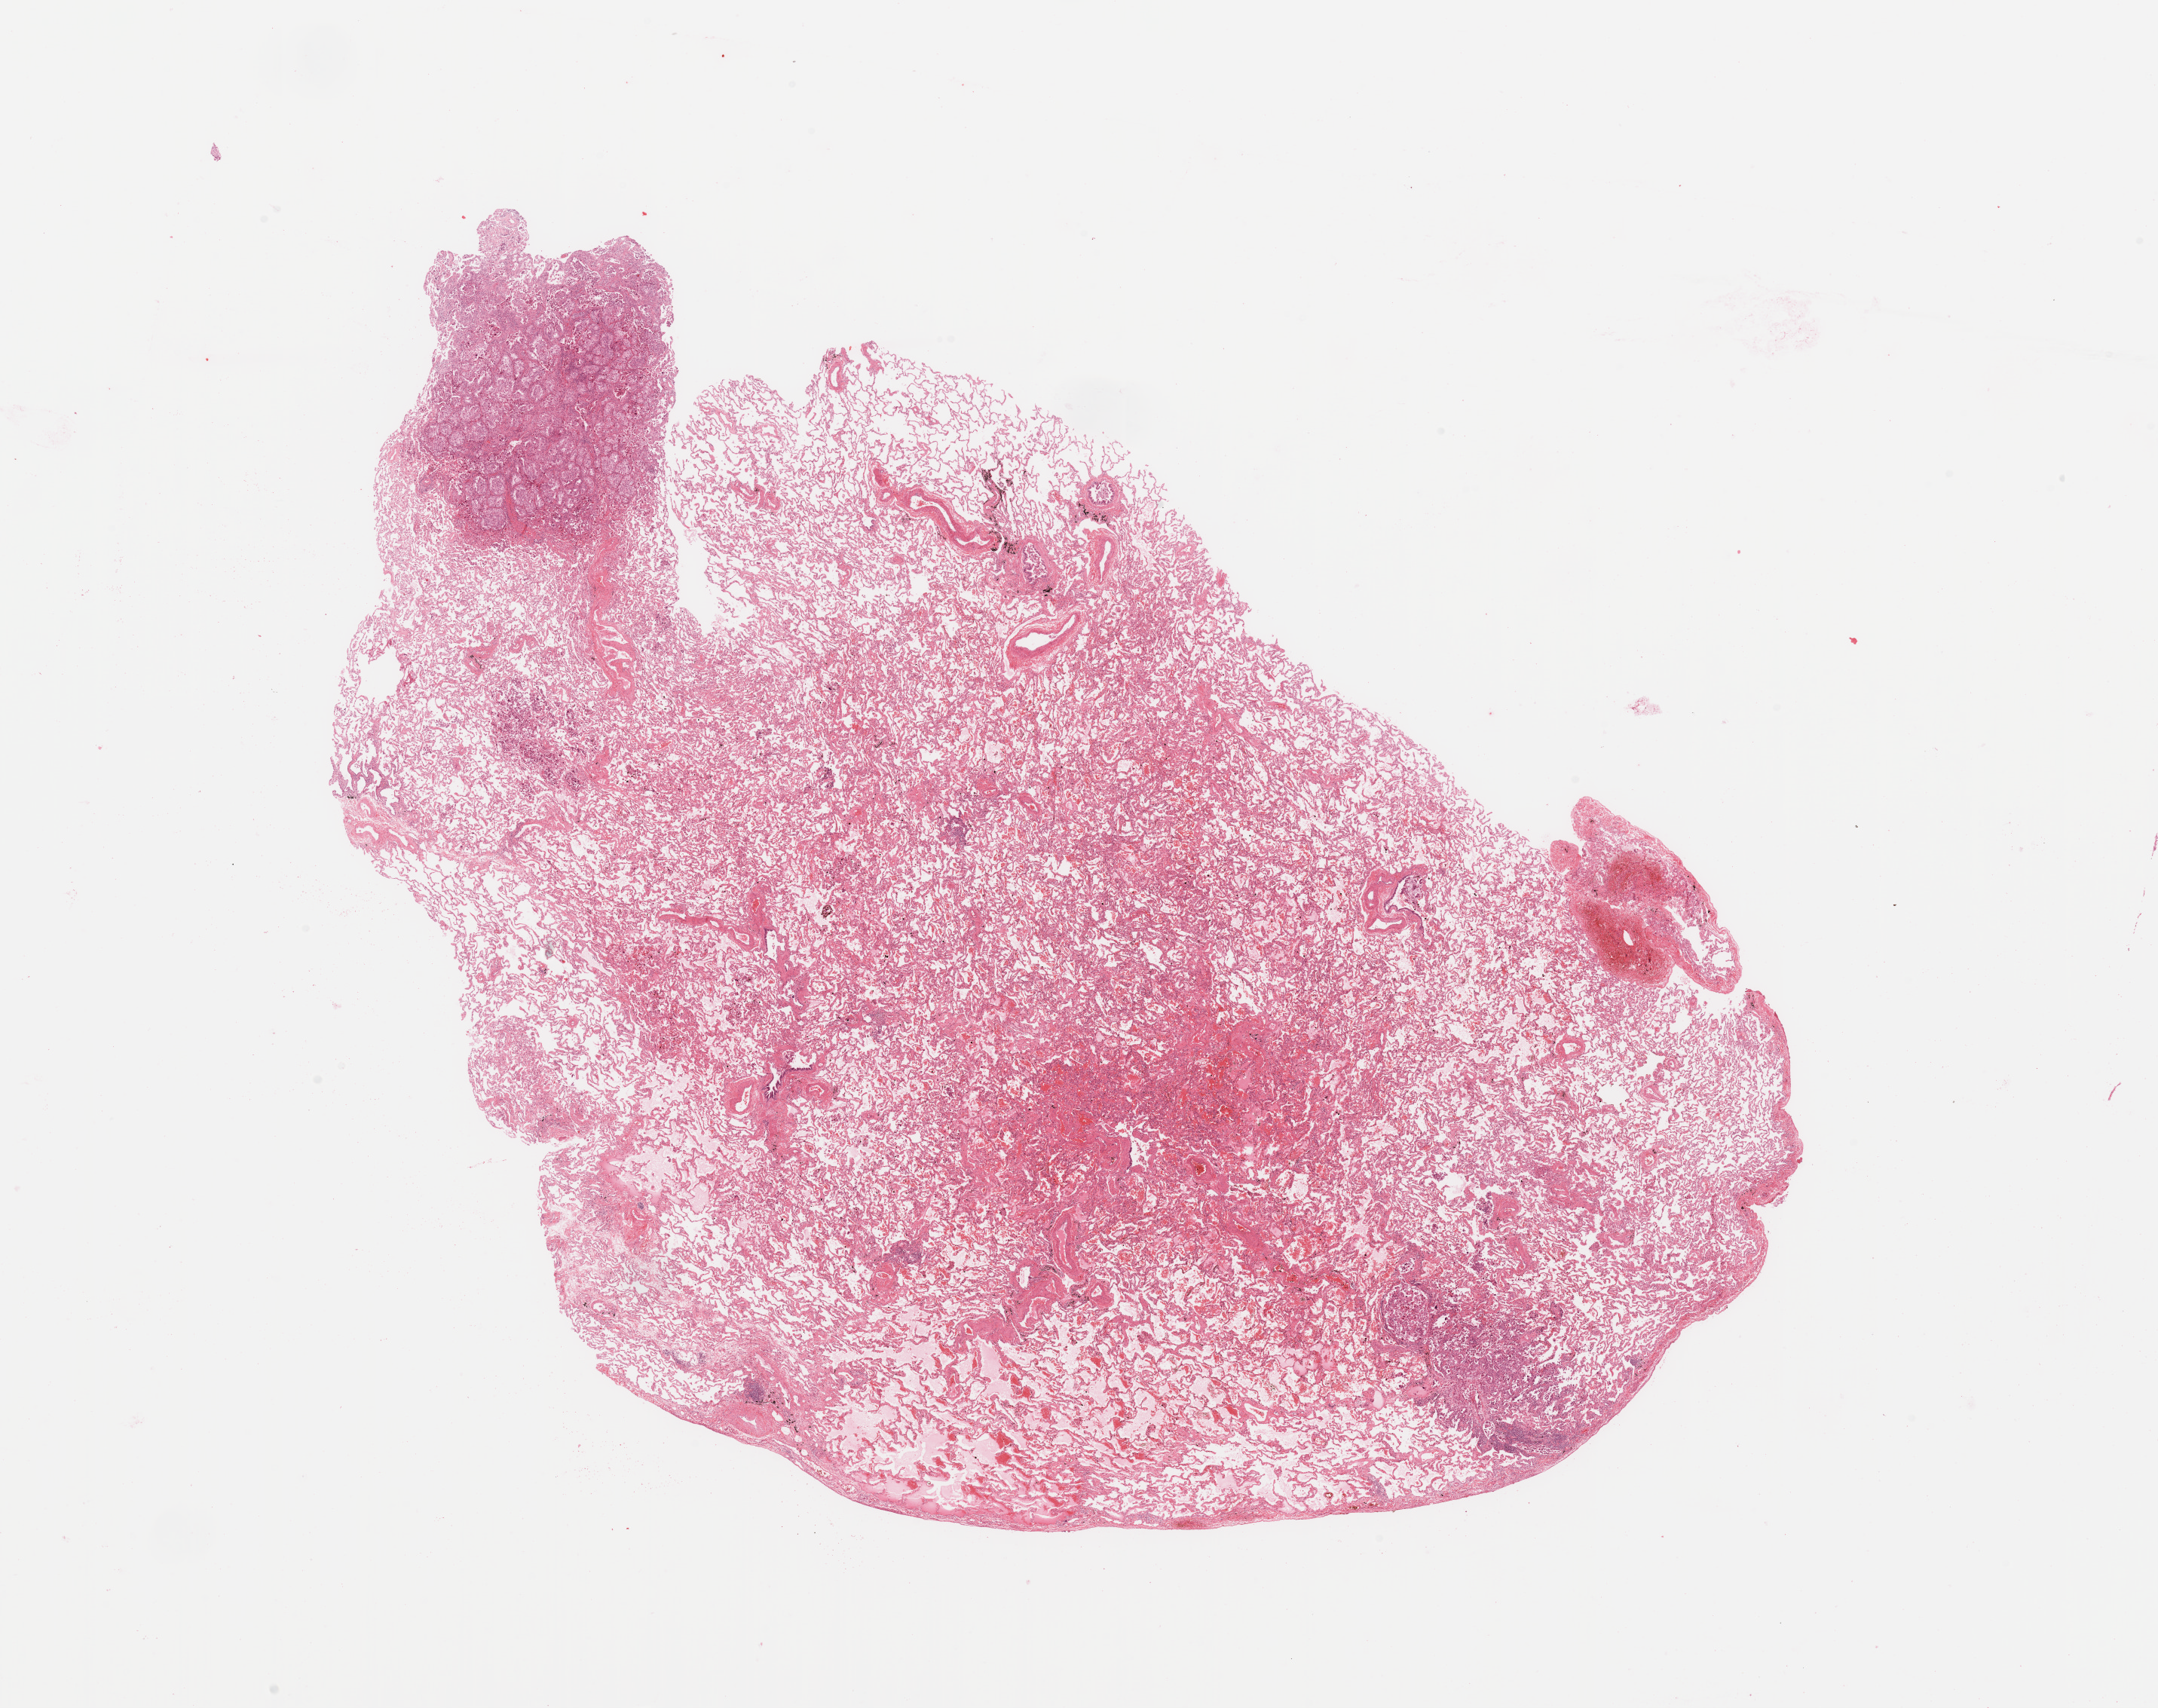
Digitized H&E-stained tissue section (whole slide), whole scanned area (about 22.6 x 17.9 mm, acquisition: 20x scan) shown as a low-resolution overview, lung, normal (non-tumour) tissue. 62-year-old female patient.
This section: normal (non-tumour) tissue from the same patient. Patient diagnosis: Adenocarcinoma, NOS.